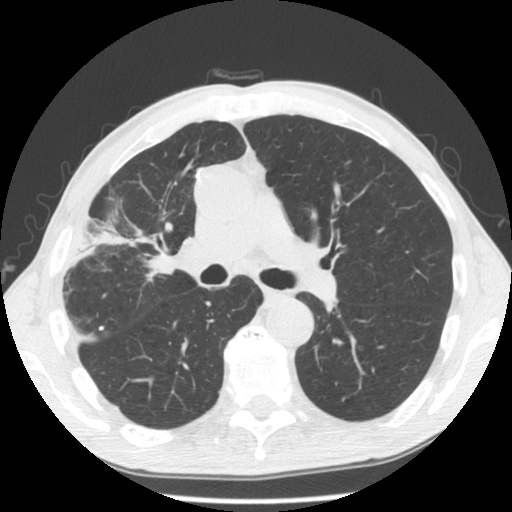
Low-dose screening chest CT, one axial slice; reconstruction kernel STANDARD; 140 kVp; lung window (W 1500 / L -600 HU); 2.5 mm slice thickness; 512 × 512 image matrix.
Annotated regions visible in this slice (expert manual segmentation):
- lesion 1 (tumor, hilum of right lung): bounding box (x1, y1, x2, y2) in pixels: (148, 253, 175, 274)